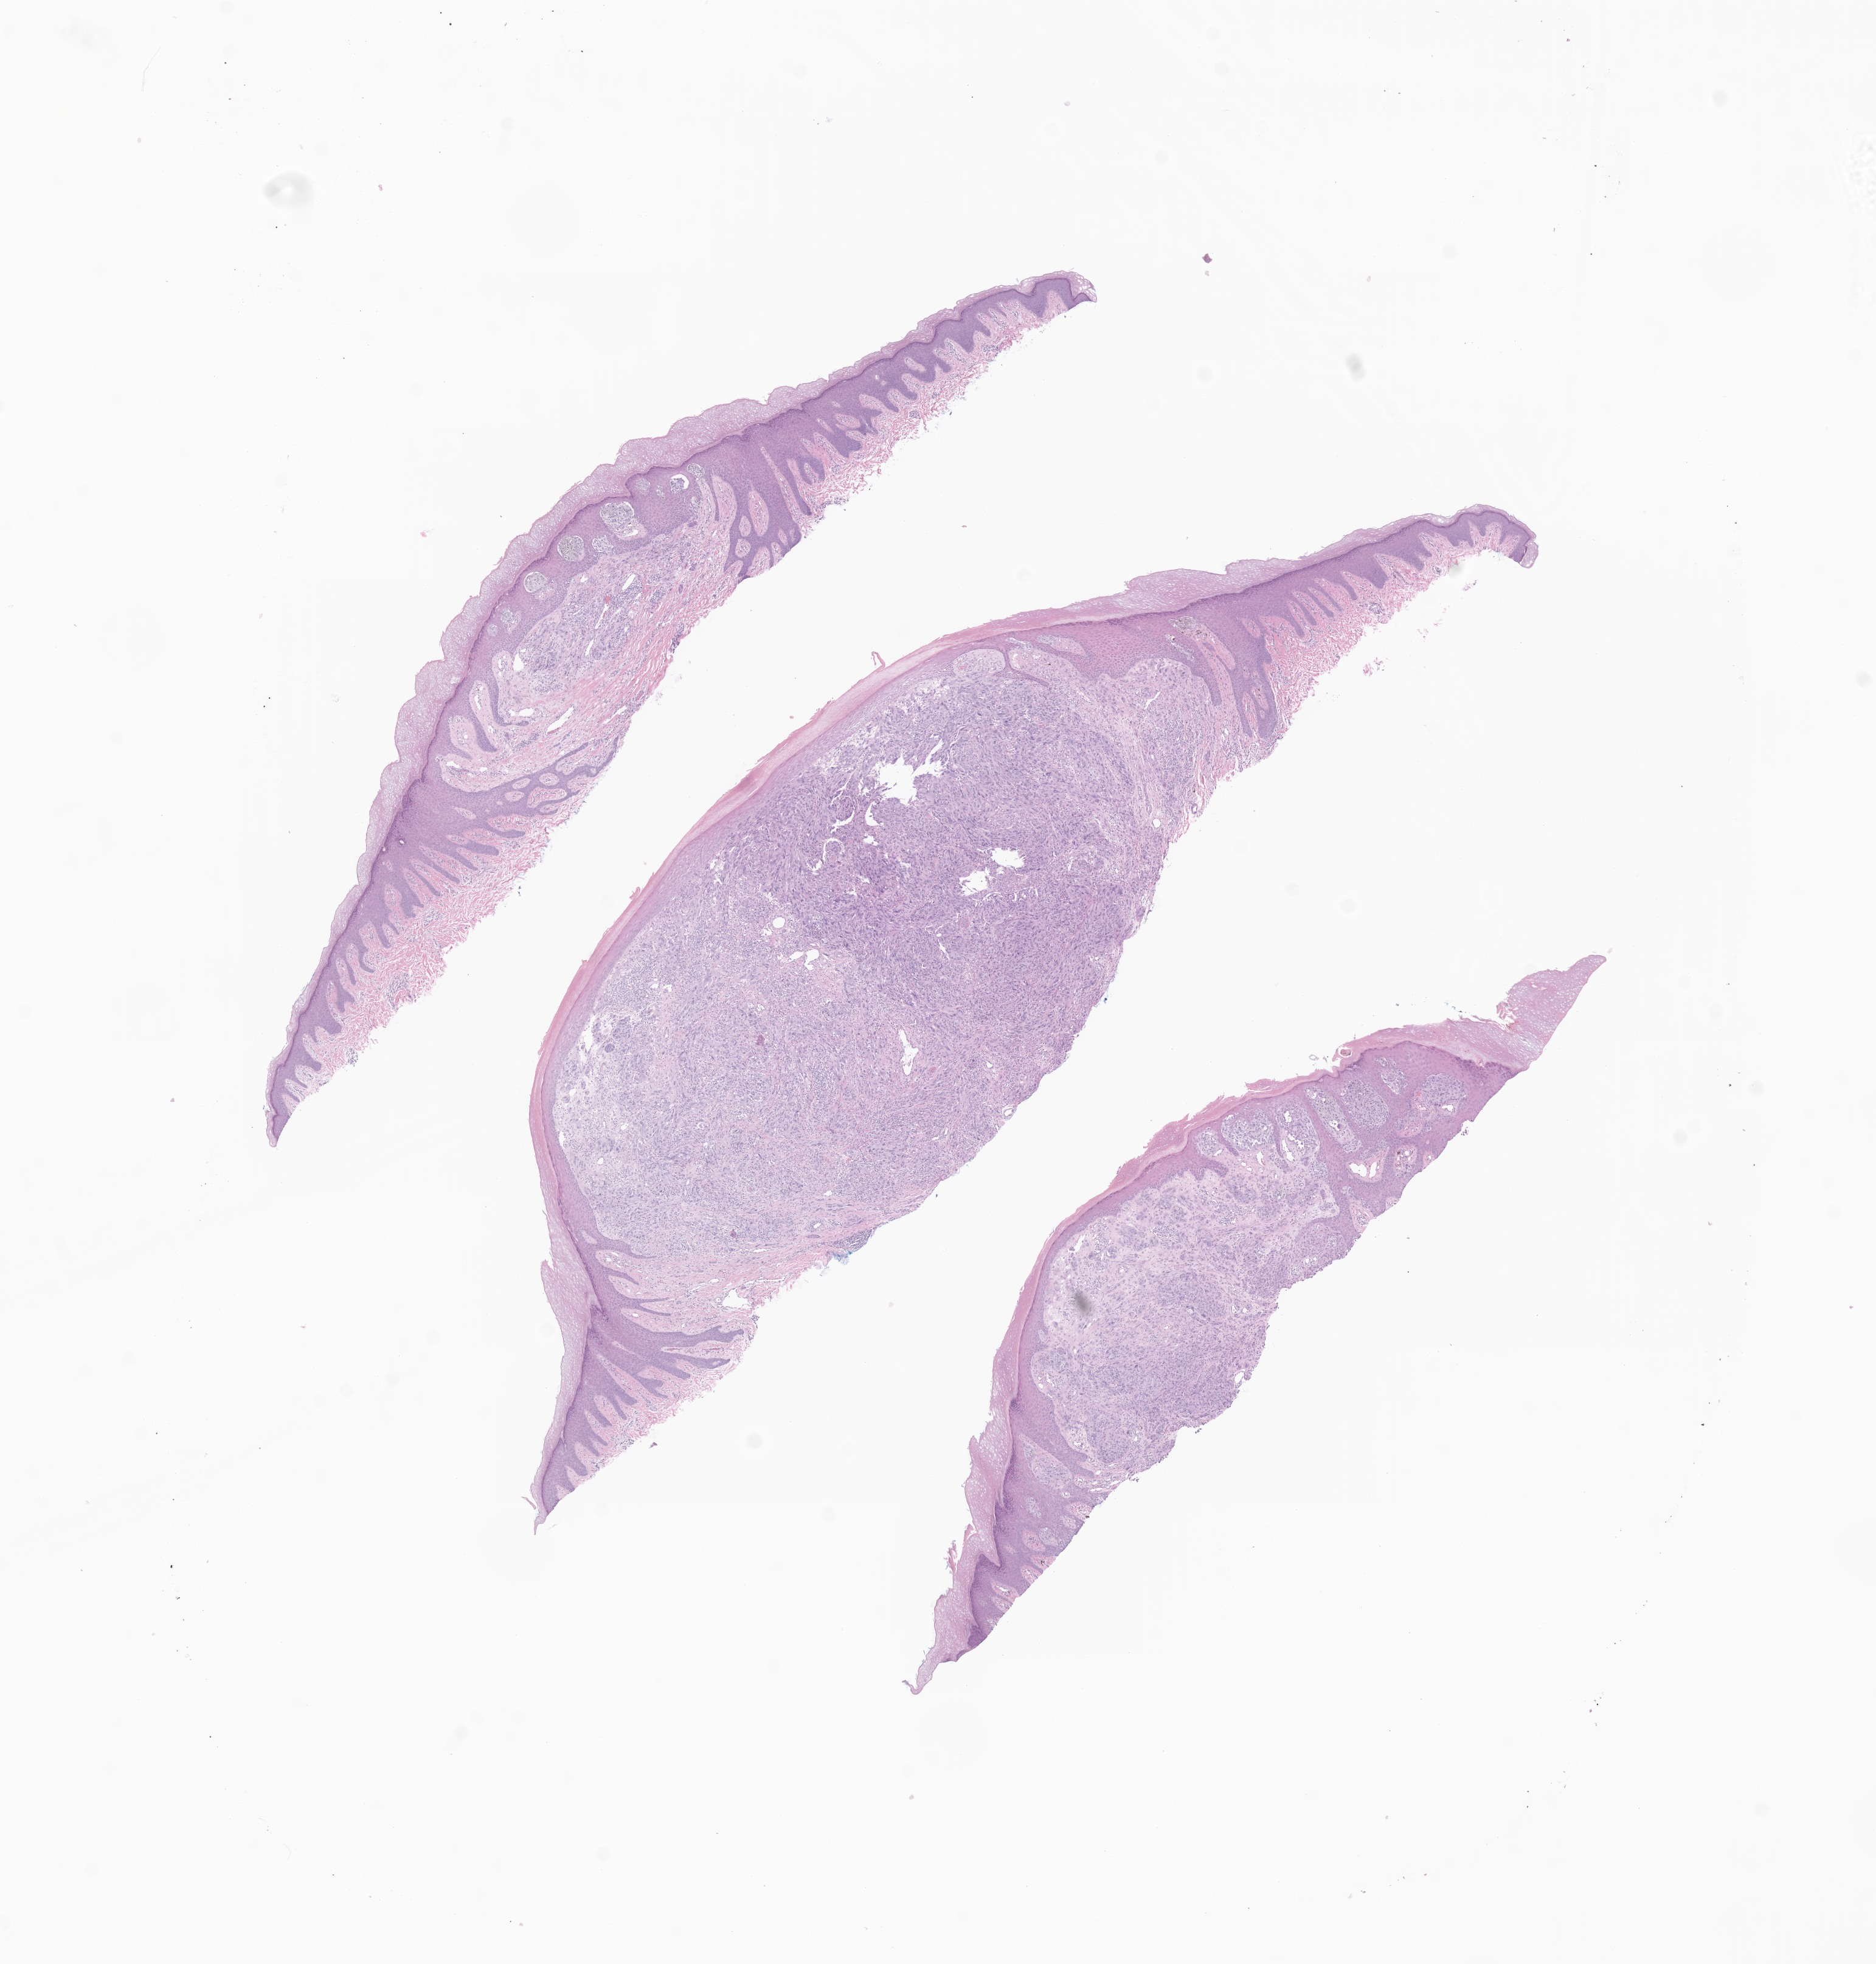
Hematoxylin and eosin (H&E) whole-slide image of tumor tissue from the skin, a low-resolution overview of the entire scanned area, about 13.0 x 13.6 mm, formalin-fixed, paraffin-embedded (FFPE) tissue. Male patient, age 159 months (13 years 3 months).
Diagnosis (ICD-O-3 morphology term): Malignant melanoma, NOS.